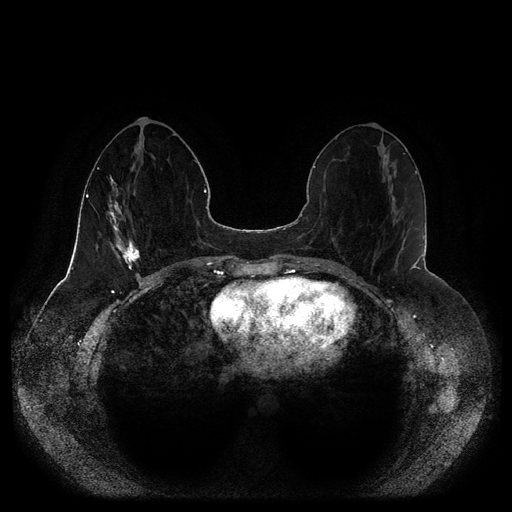
Breast MRI (dynamic contrast-enhanced, multi-phase), one axial slice. Position 40 of 116 along the scan axis. Dynamic contrast-enhanced series, time point 2 of 5 at this slice position (early post-contrast). 1.5 T. TE 2.5 ms, TR 5.2 ms. 512 × 512 image matrix, field of view 390 × 390 mm. Patient: female, 44 years.
Structures marked on this image (semi-automatic segmentation, software-assisted and operator-edited):
- breast lesion (labelled 'tumour' in the annotation; benign lesions carry a separate 'benign' label): box from (x=115, y=238) to (x=140, y=270) px
- breast lesion (labelled 'tumour' in the annotation; benign lesions carry a separate 'benign' label): (x=108, y=175)–(x=123, y=238)